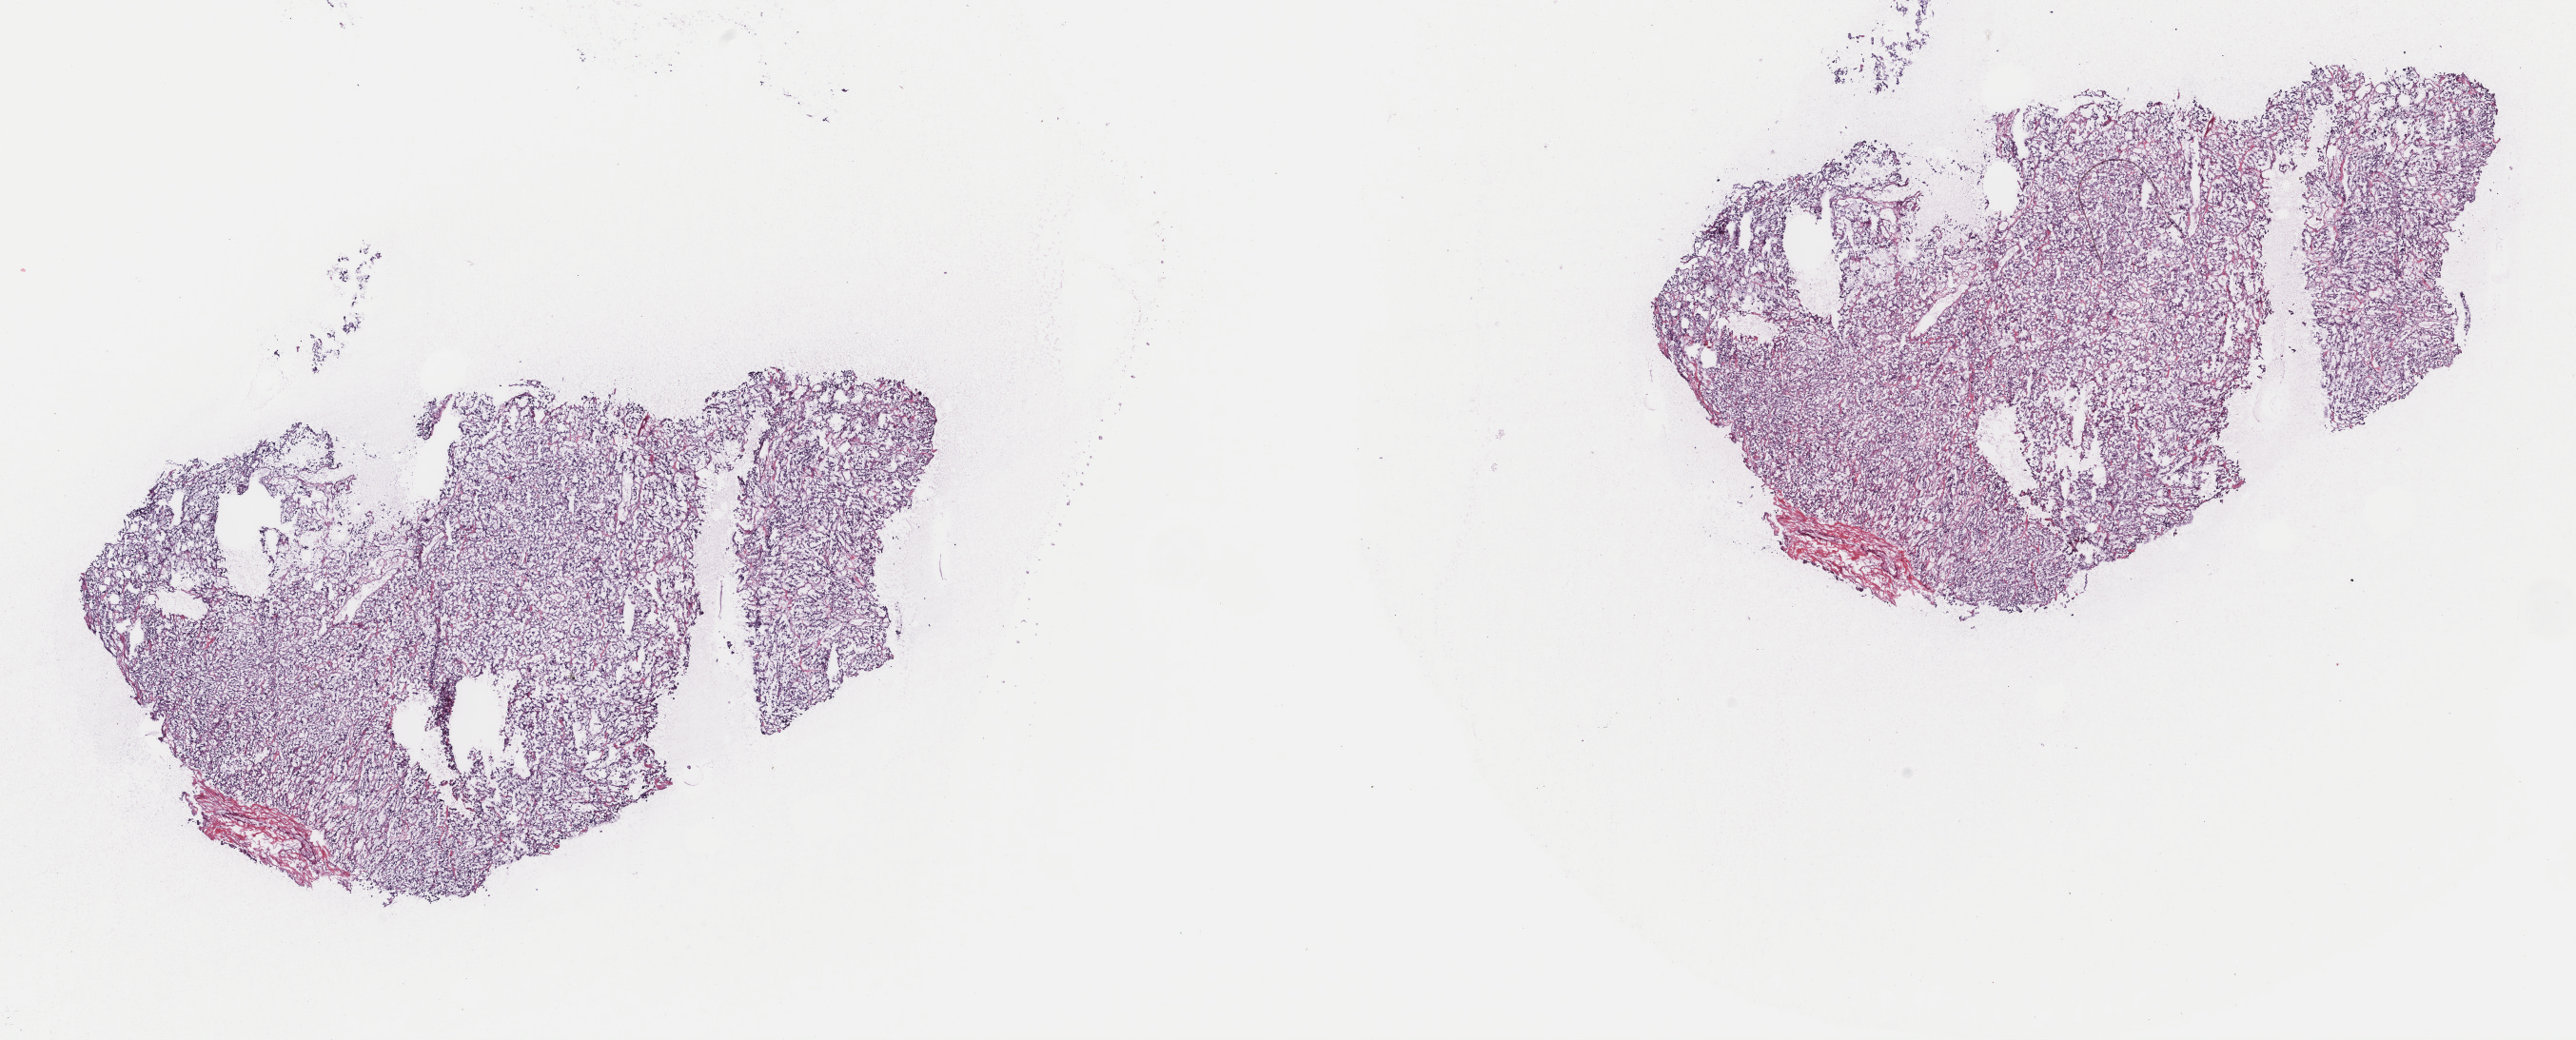
Digitized H&E-stained tissue section (whole slide) — shown as a low-resolution overview of the whole scanned area (about 21.5 x 8.7 mm); frozen section from the top of the tissue portion; retroperitoneum and peritoneum, primary tumour sample. Male, age 24 years at initial diagnosis. Slide review estimates, as recorded: tumour cells 90%, tumour nuclei 100%, normal cells 0%, stromal cells 10%, necrosis 0%. Inflammatory infiltration, as recorded: lymphocyte infiltration 0%, monocyte infiltration 0%, neutrophil infiltration 0%.
Diagnosis: Extra-adrenal paraganglioma, NOS (retroperitoneum).